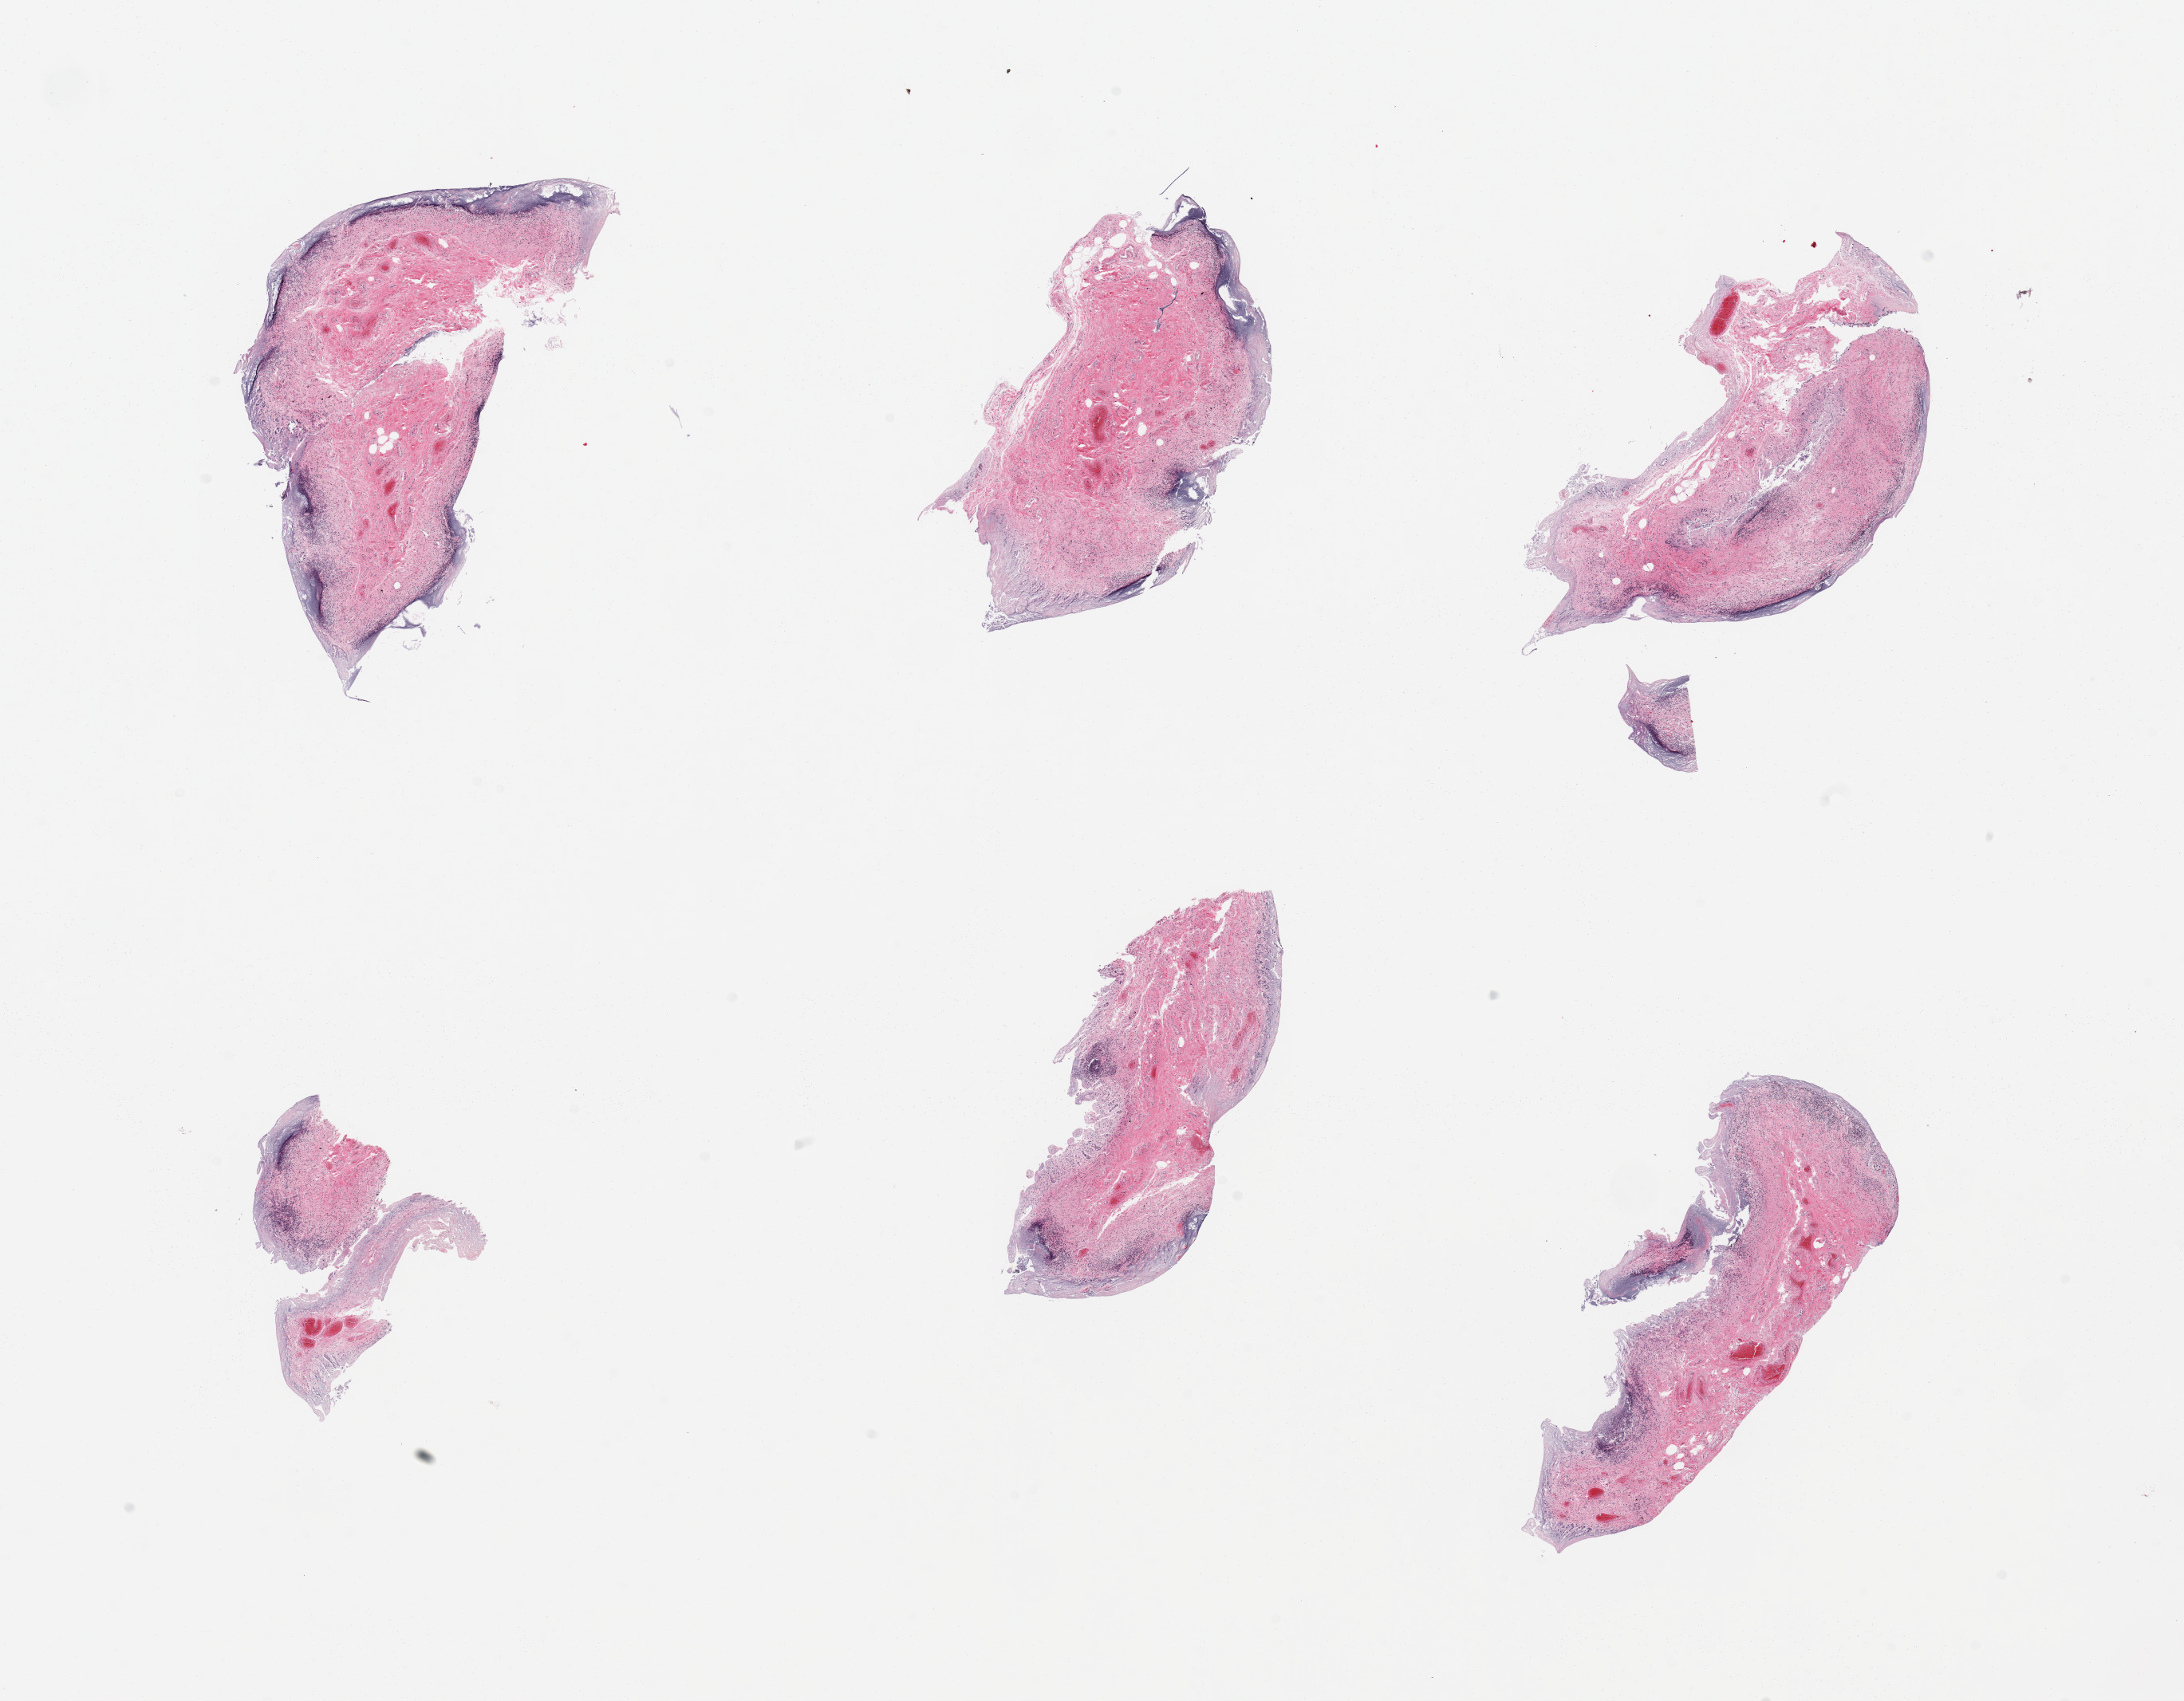
Whole-slide image, H&E stain, brightfield, low-resolution overview of the scanned area, about 21.7 x 16.9 mm; PAXgene-fixed paraffin-embedded (PFPE) section; section of ileum (target tissue); donor tissue sample.
Pathologist's review note for this sample: 6 pieces, 5-10% lymphoid aggregates, advanced autolysis.